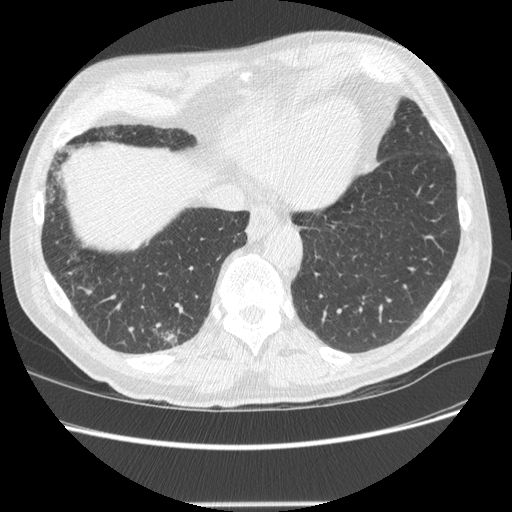
Low-dose screening chest CT, one axial slice; slice 57 of 245 in the series (ordered by position); reconstruction kernel STANDARD; 120 kVp; lung window (W 1500 / L -600 HU); 1.25 mm slice thickness; 512 × 512 image matrix, field of view 372 × 372 mm.
Structures marked on this image (outlined manually by an expert reader):
- lesion 1 (tumor, lower lobe of right lung): bounding box <163,334,176,343> (left, top, right, bottom; pixels)